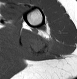
MRI of an extremity soft-tissue mass, one axial slice; position 7 of 28 along the scan axis; MR volume resampled by the dataset authors to the PET/CT grid (not the native acquisition matrix); 3.27 mm slice thickness; 77 × 79 image matrix, field of view 75 × 77 mm. Female patient. From the clinical record (not read from this slice): histological type: malignant fibrous histiocytoma; grade: low; site of the primary tumour: left arm.
Structures marked on this image (expert contour drawn on MRI and transferred to this co-registered scan by the dataset authors):
- gross tumour volume (mass): bounding box [x1, y1, x2, y2] px = [28, 31, 54, 58]